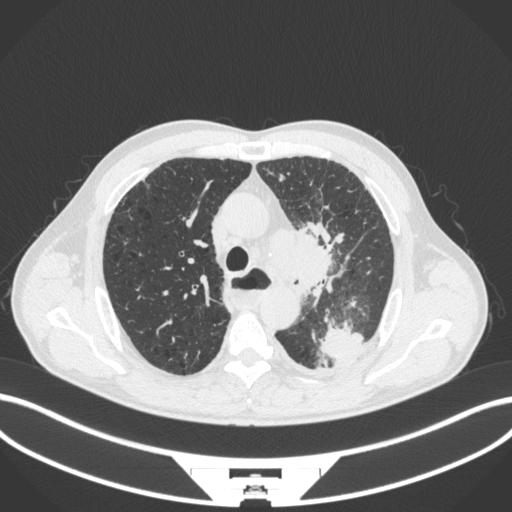
Chest CT, one axial slice; position 275 of 411 along the scan axis; reconstruction kernel B31f; 120 kVp; lung window (W 1500 / L -600 HU); 512 × 512 image matrix, field of view 400 × 400 mm. Male patient, age 57 years. Case-level facts recorded for this patient, not image findings: clinical TNM (as recorded): T2a N1 M0.
Outlined on this slice (bounding box drawn by a radiologist):
- lung tumour (recorded histology: squamous cell carcinoma): bounding box [x1, y1, x2, y2] px = [263, 220, 337, 293]